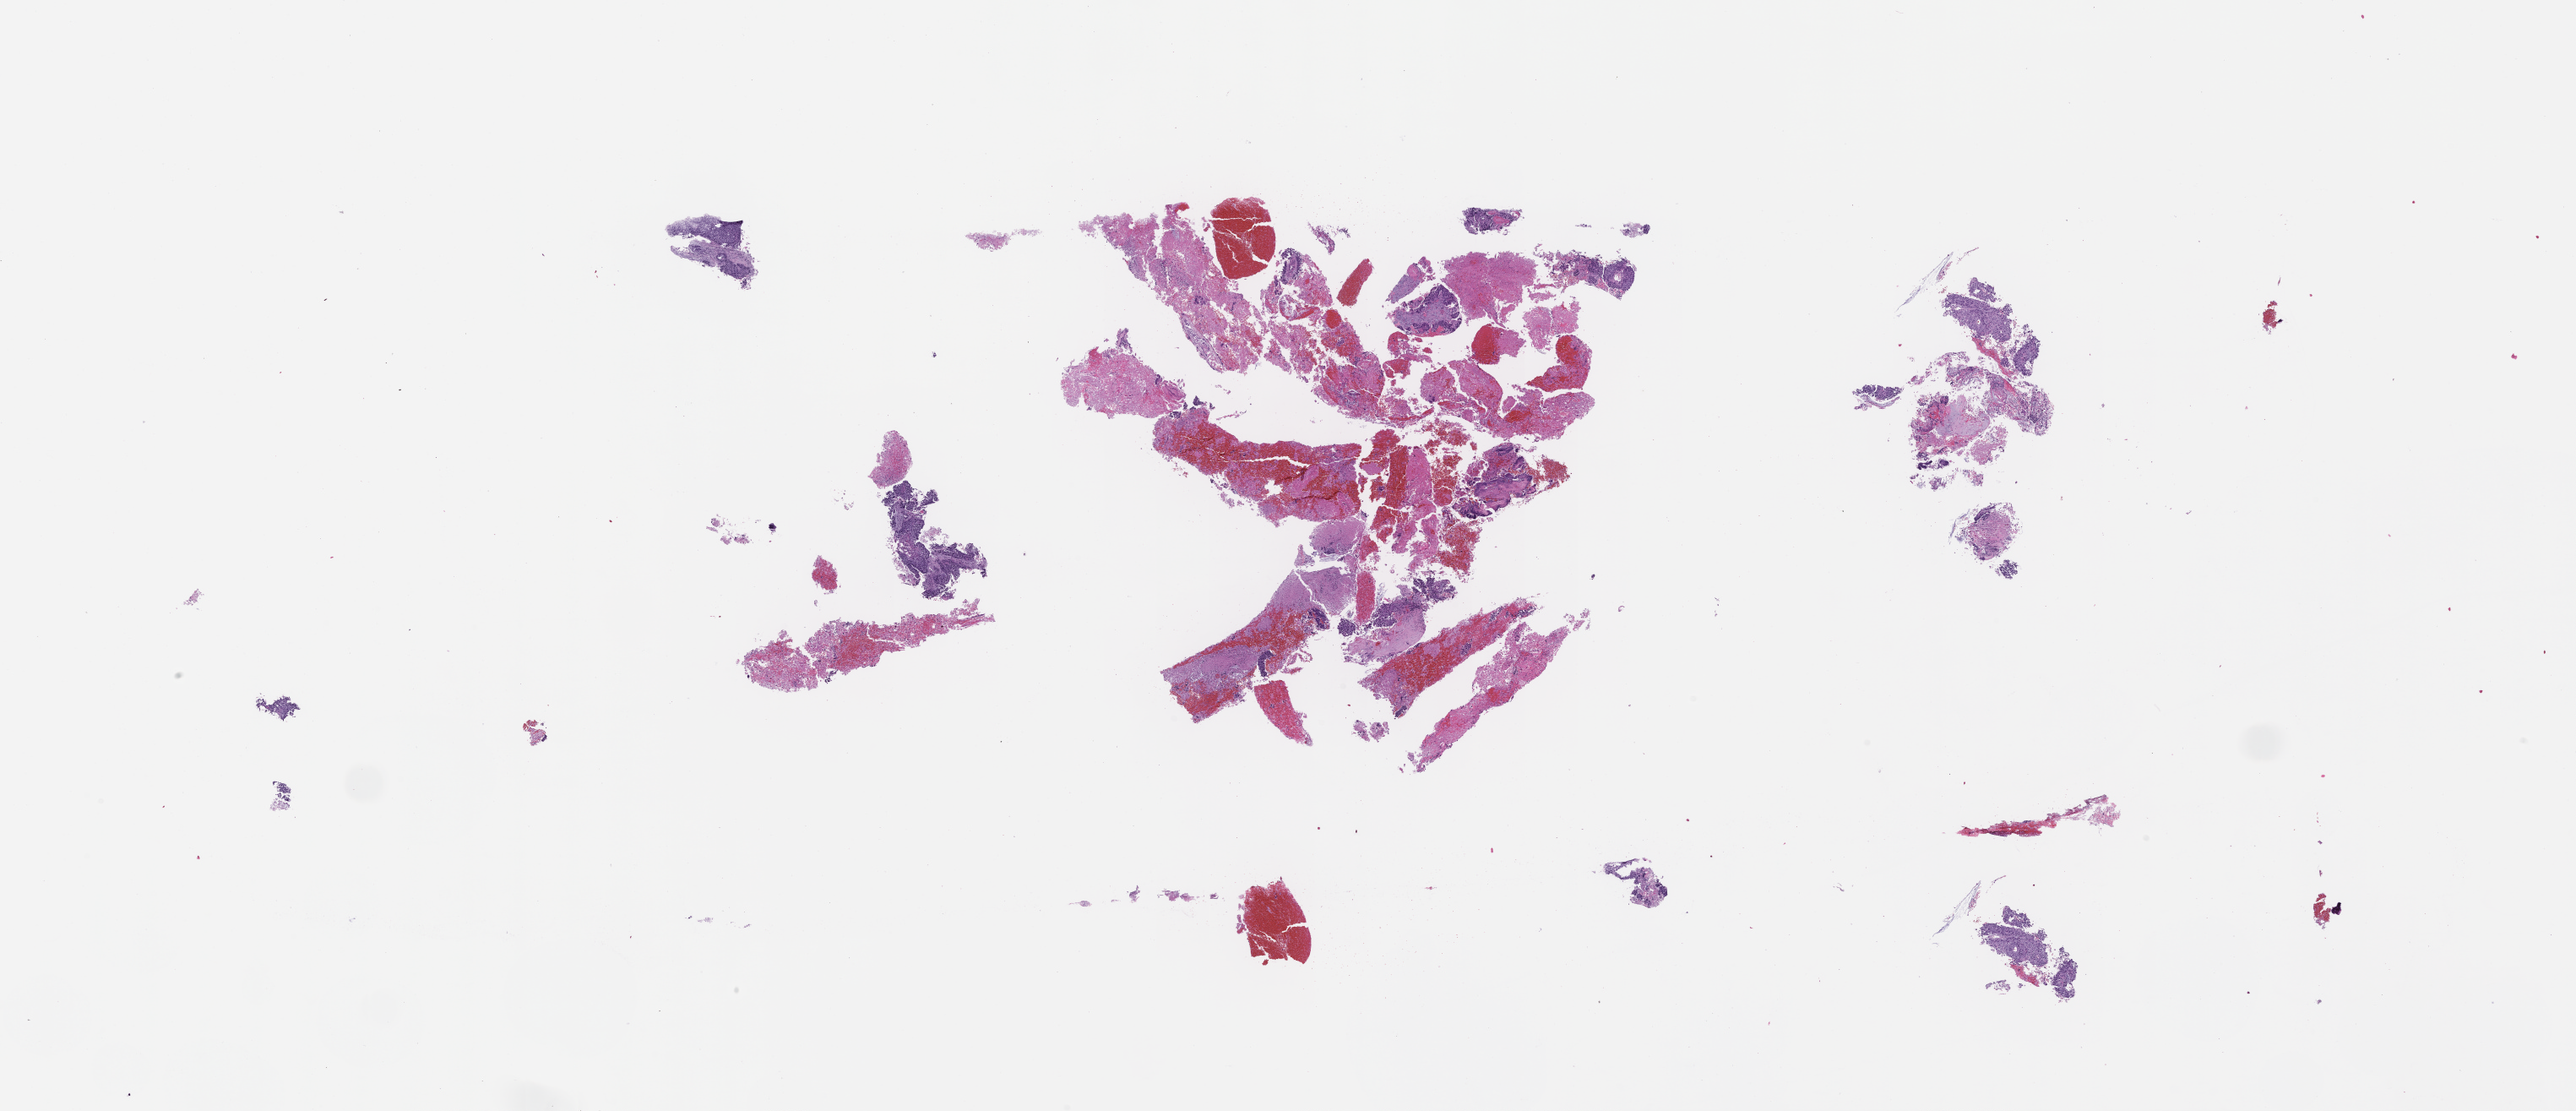
Whole-slide image, hematoxylin and eosin (H&E) stain — a low-resolution overview of the entire scanned area, about 24.6 x 10.6 mm, formalin-fixed, paraffin-embedded (FFPE) tissue, specimen time point: archival tissue. Patient sex: male.
* this section: metastasis (sampled organ not recorded)
* patient diagnosis (primary): Non-Small Cell Lung Carcinoma